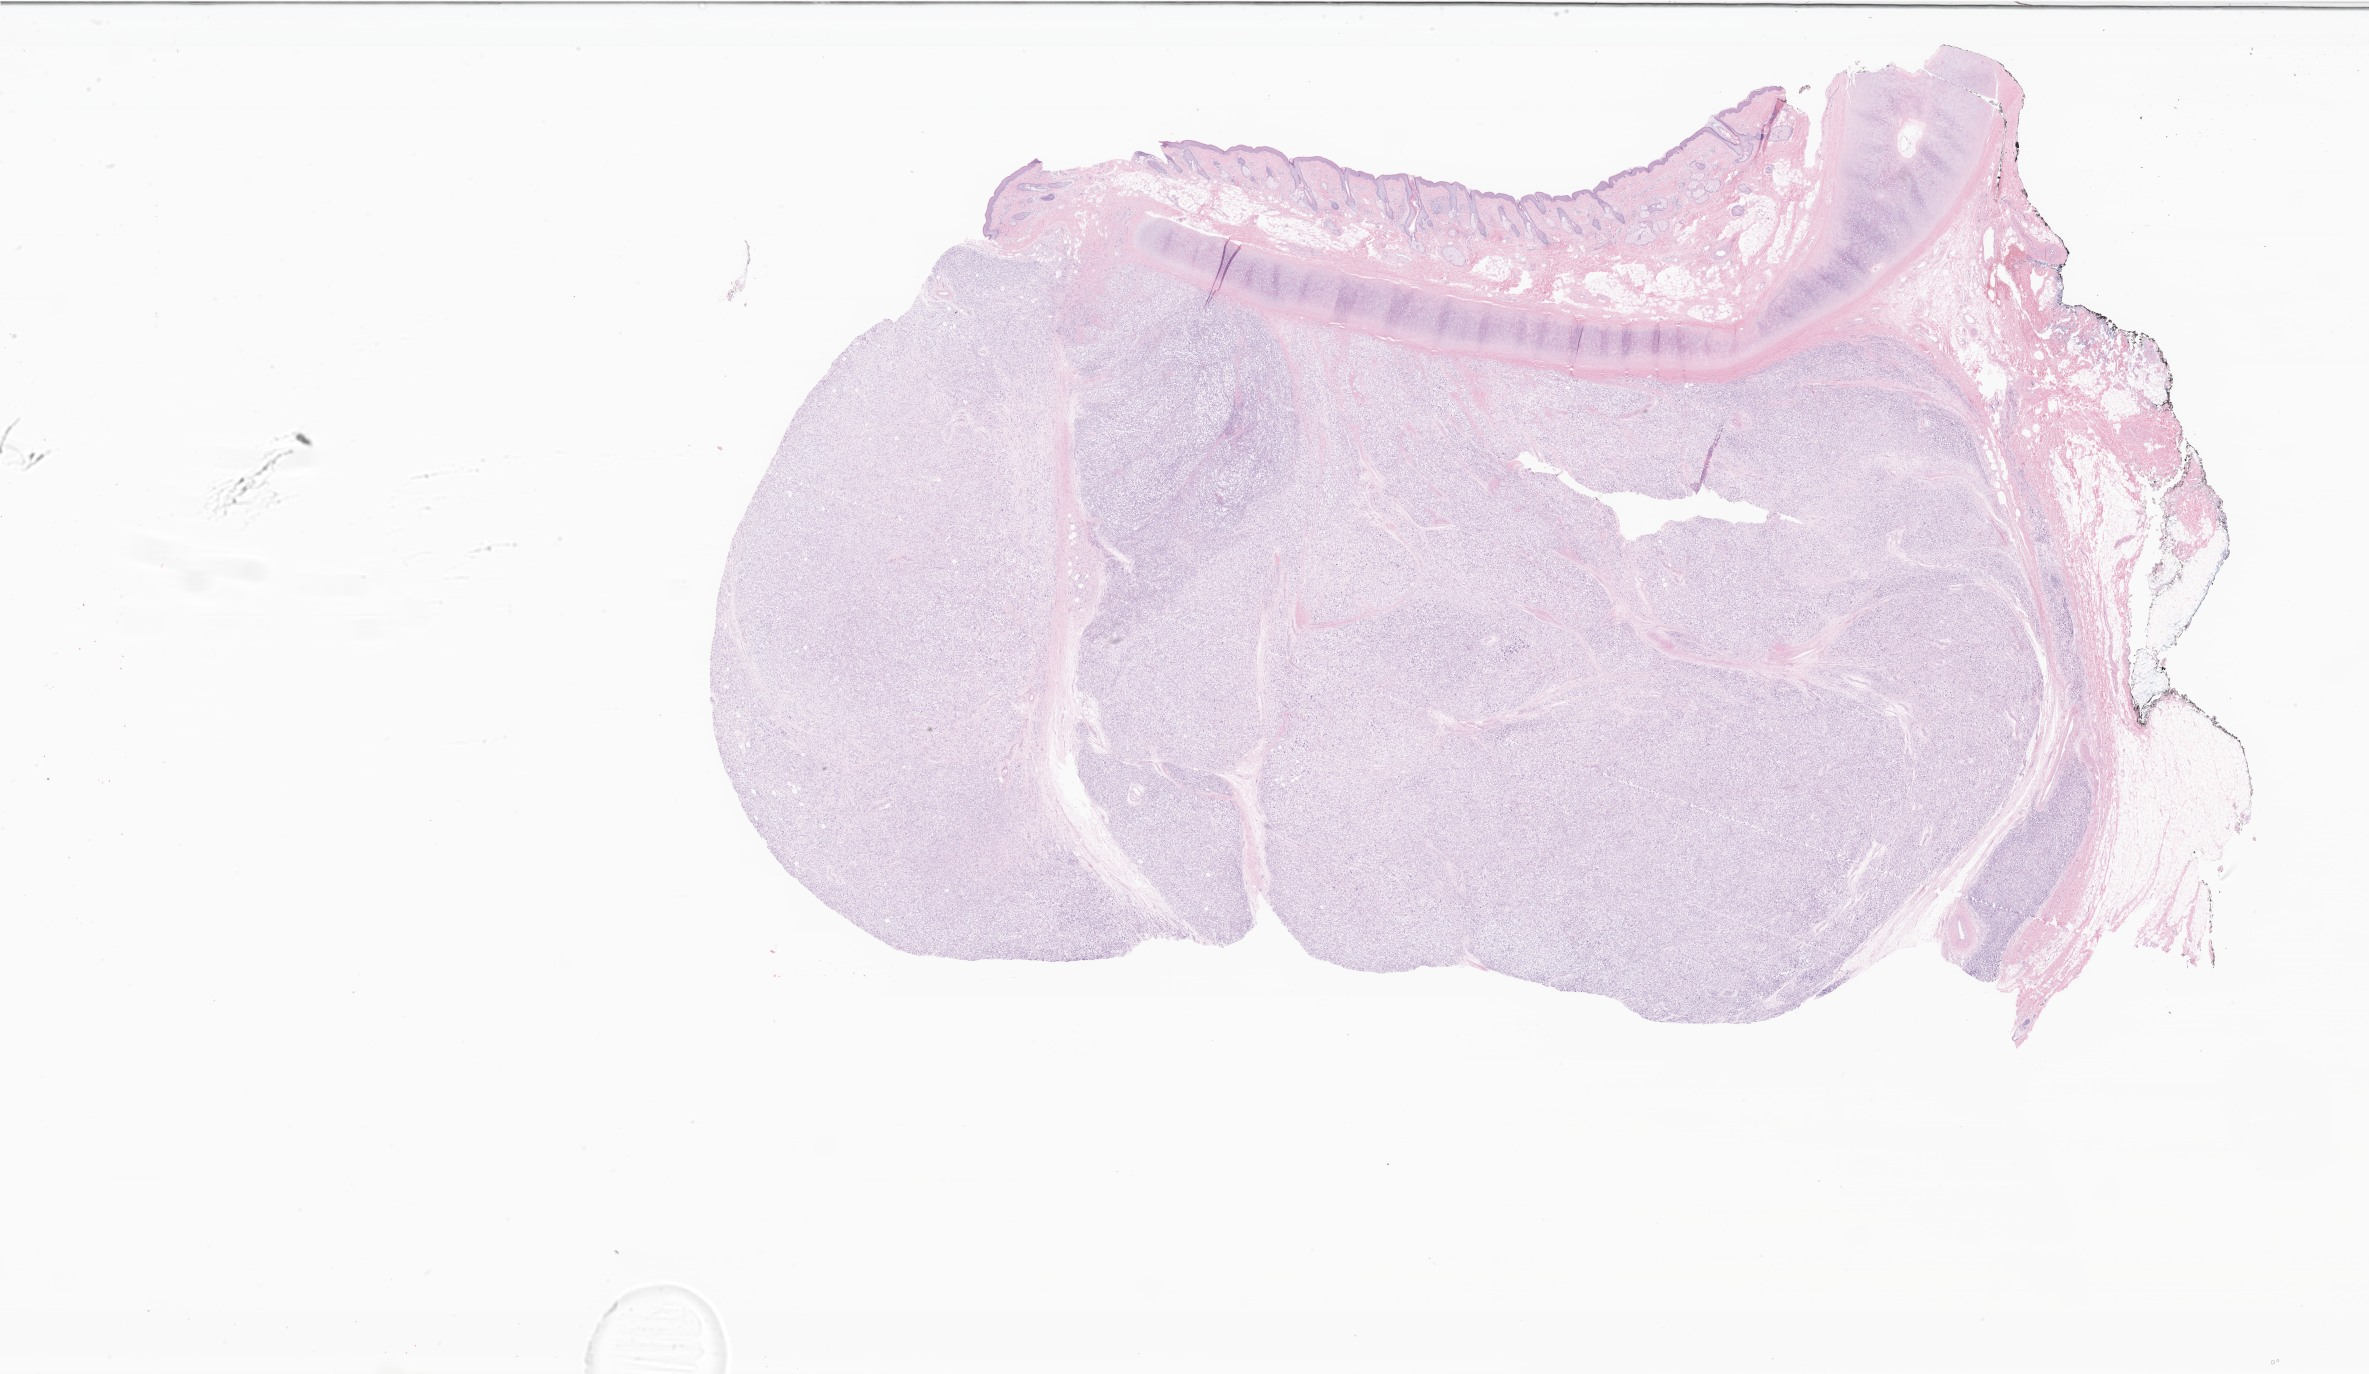
Whole-slide image, H&E stain of tumor tissue from the external ear — a low-resolution overview of the entire scanned area, about 40.0 x 23.2 mm, formalin-fixed, paraffin-embedded (FFPE) tissue. Female patient, age 223 months (18 years 7 months).
* diagnosis (ICD-O-3 morphology term): Embryonal rhabdomyosarcoma, NOS